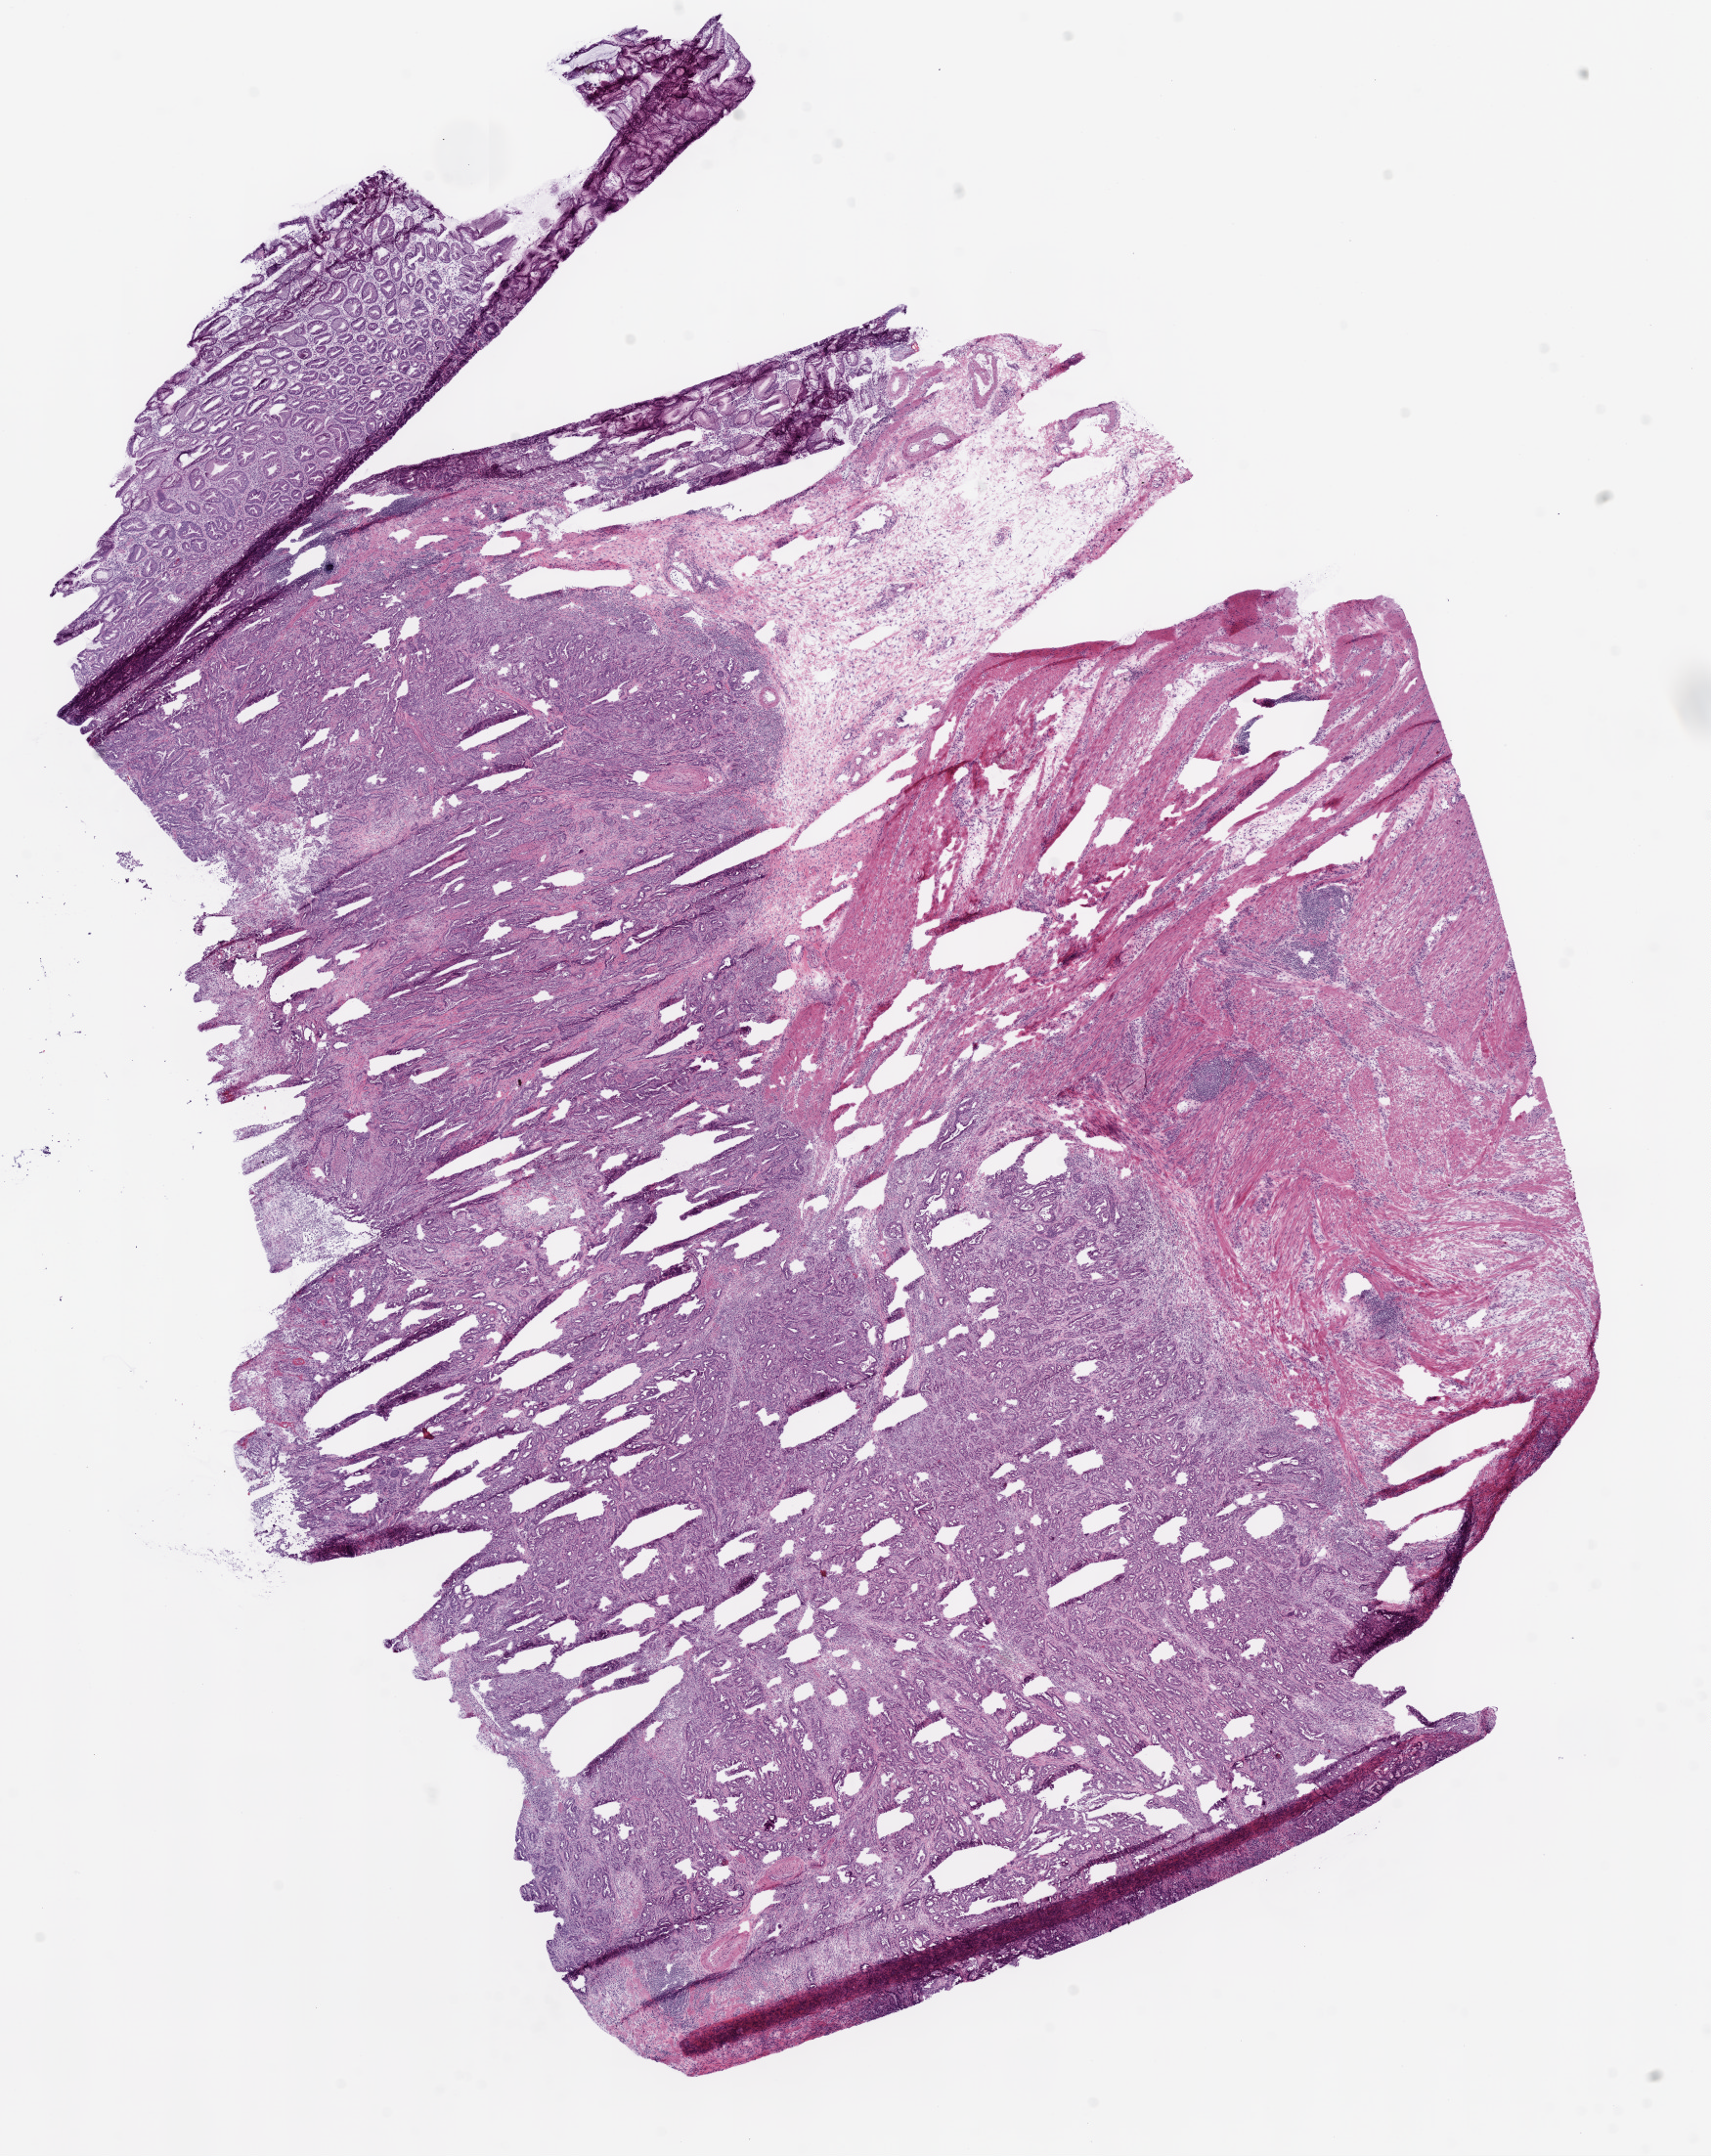
Whole-slide histology image, H&E — a low-resolution overview of the entire scanned area, about 14.0 x 17.7 mm. Frozen section from the top of the tissue portion. Sample: primary tumour, stomach. Female, age 74 years at initial diagnosis. Histologic grade: G2 (moderately differentiated). Pathologist review of this section (percent, as recorded): tumour cells 65%, tumour nuclei 65%, normal cells 25%, stromal cells 5%, necrosis 5%.
• histologic diagnosis: Adenocarcinoma, NOS (gastric antrum)